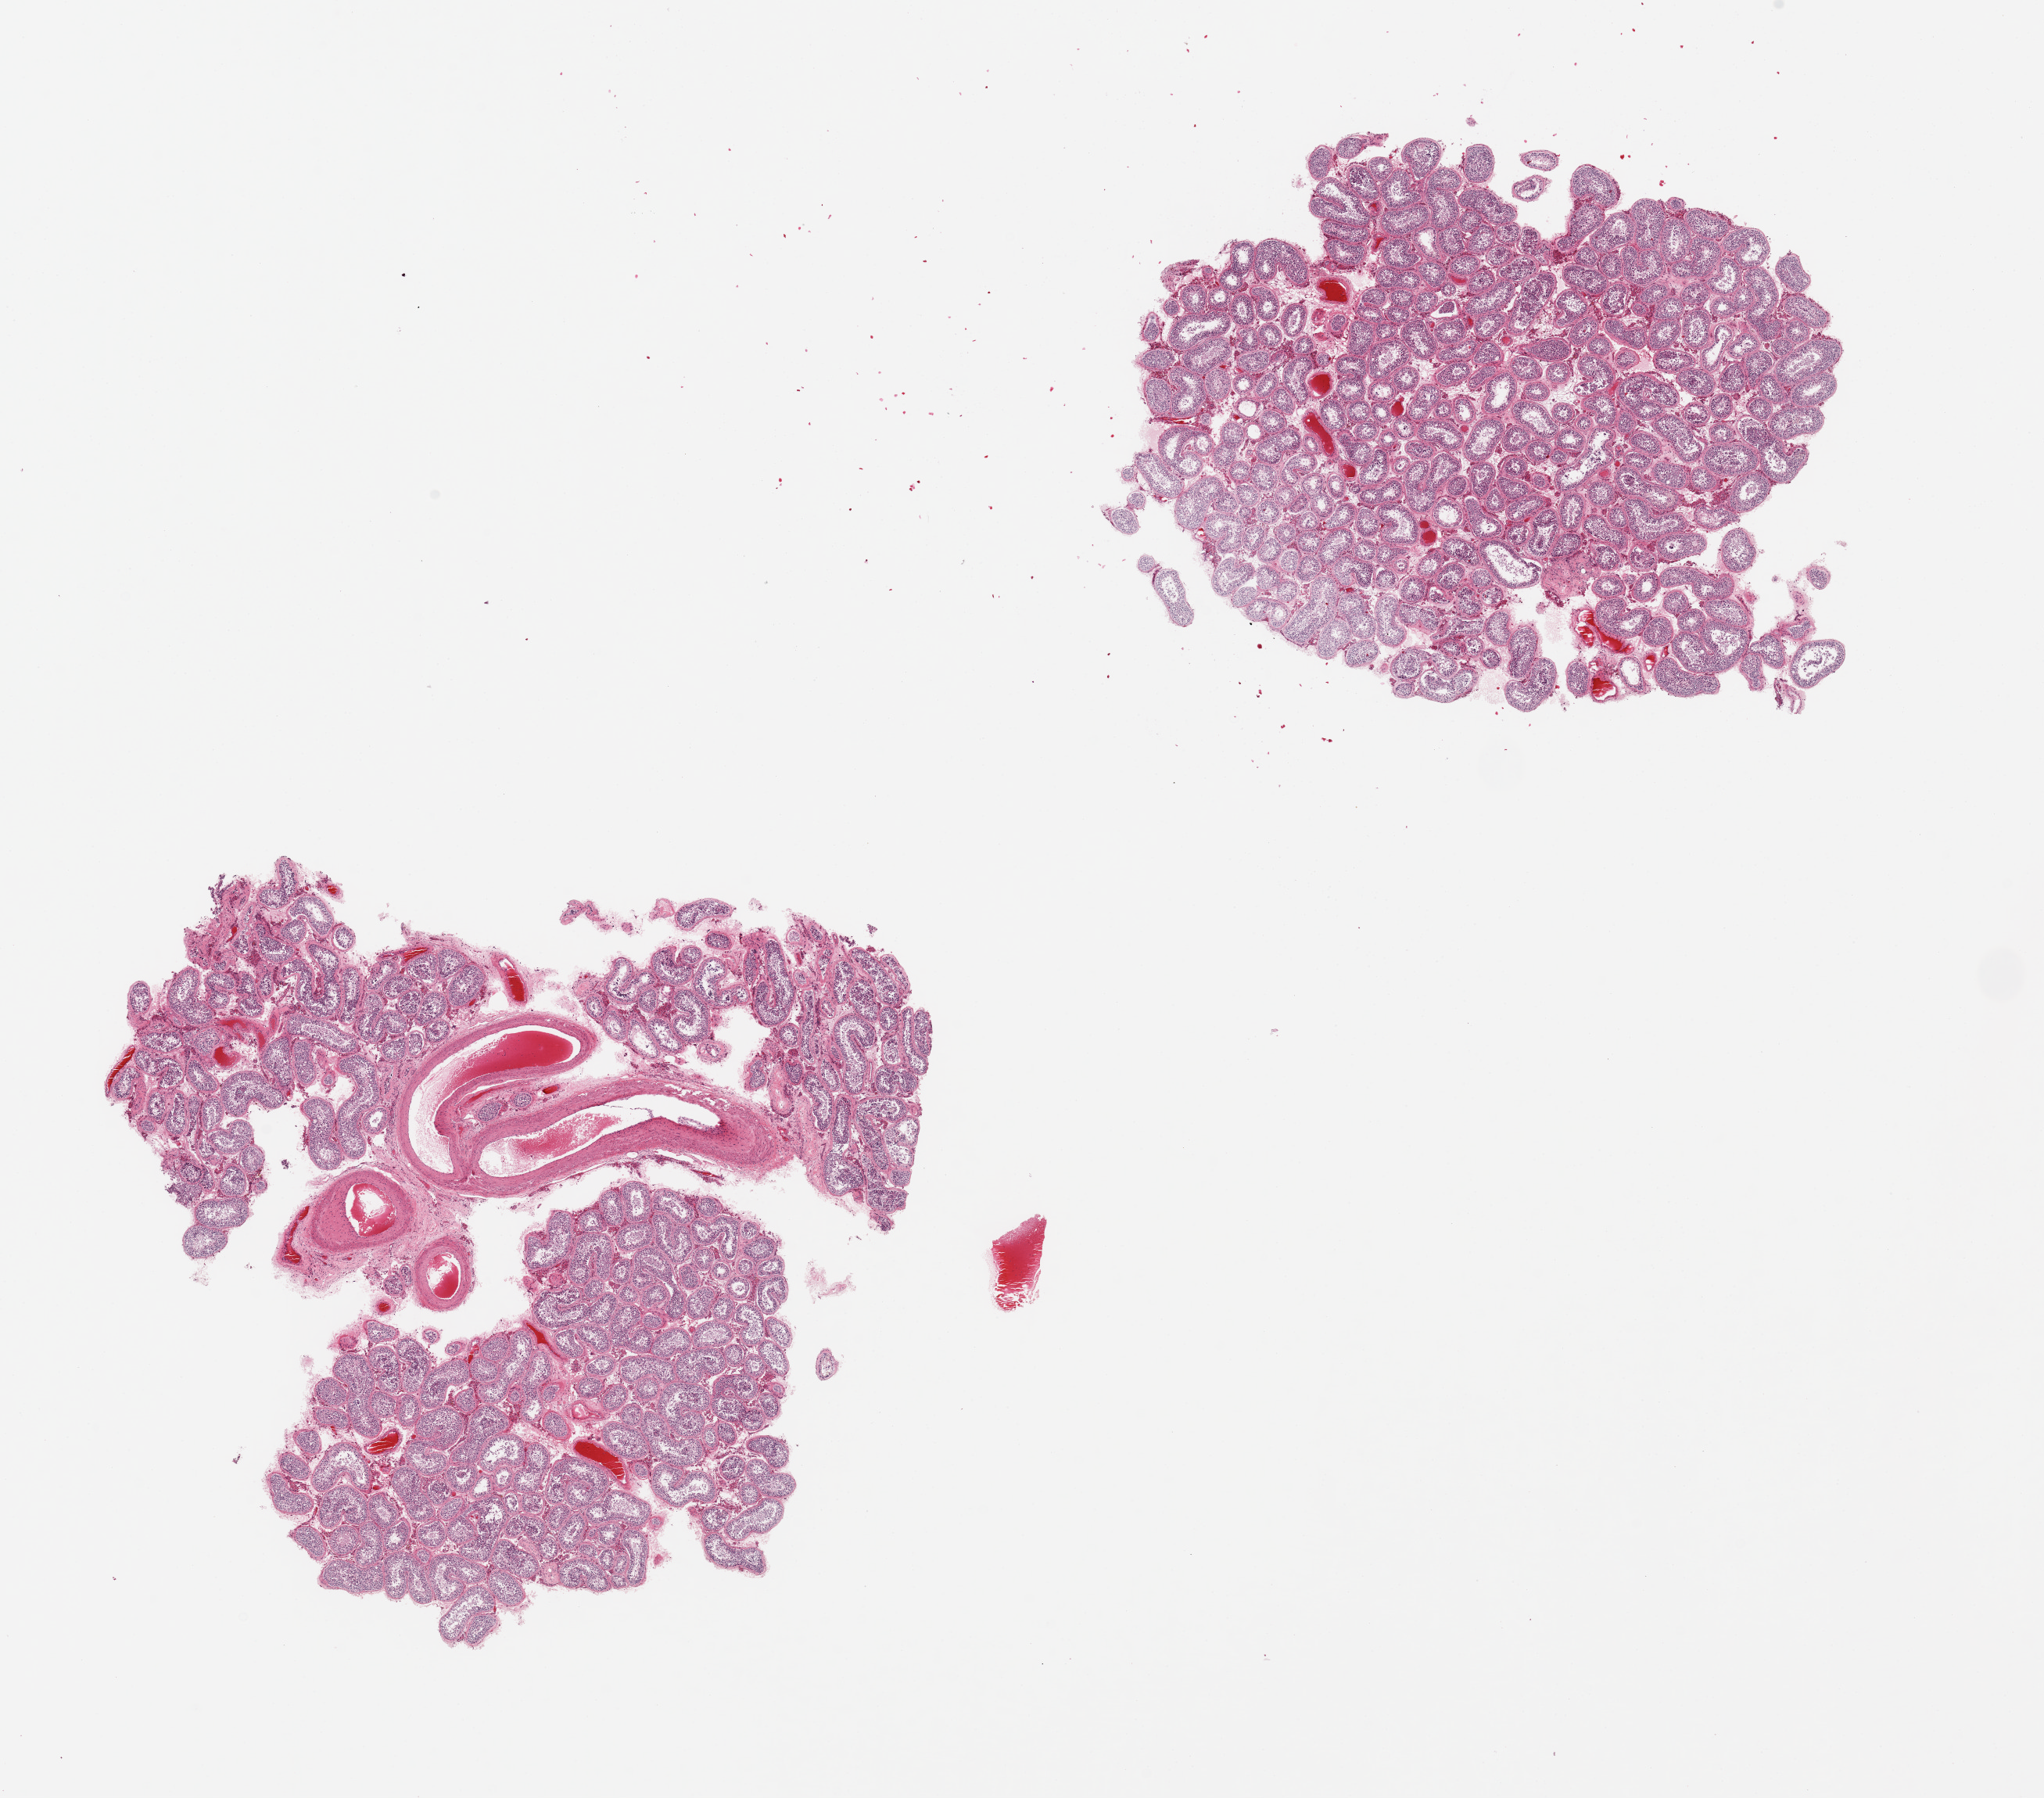
Digitized haematoxylin and eosin-stained section, low-resolution overview of the scanned area, about 20.7 x 18.2 mm. PAXgene-fixed paraffin-embedded (PFPE) section. Target tissue: testis. Donor tissue sample. Donor: male.
Pathologist's review note for this sample: 2 pieces, prominent vessels.